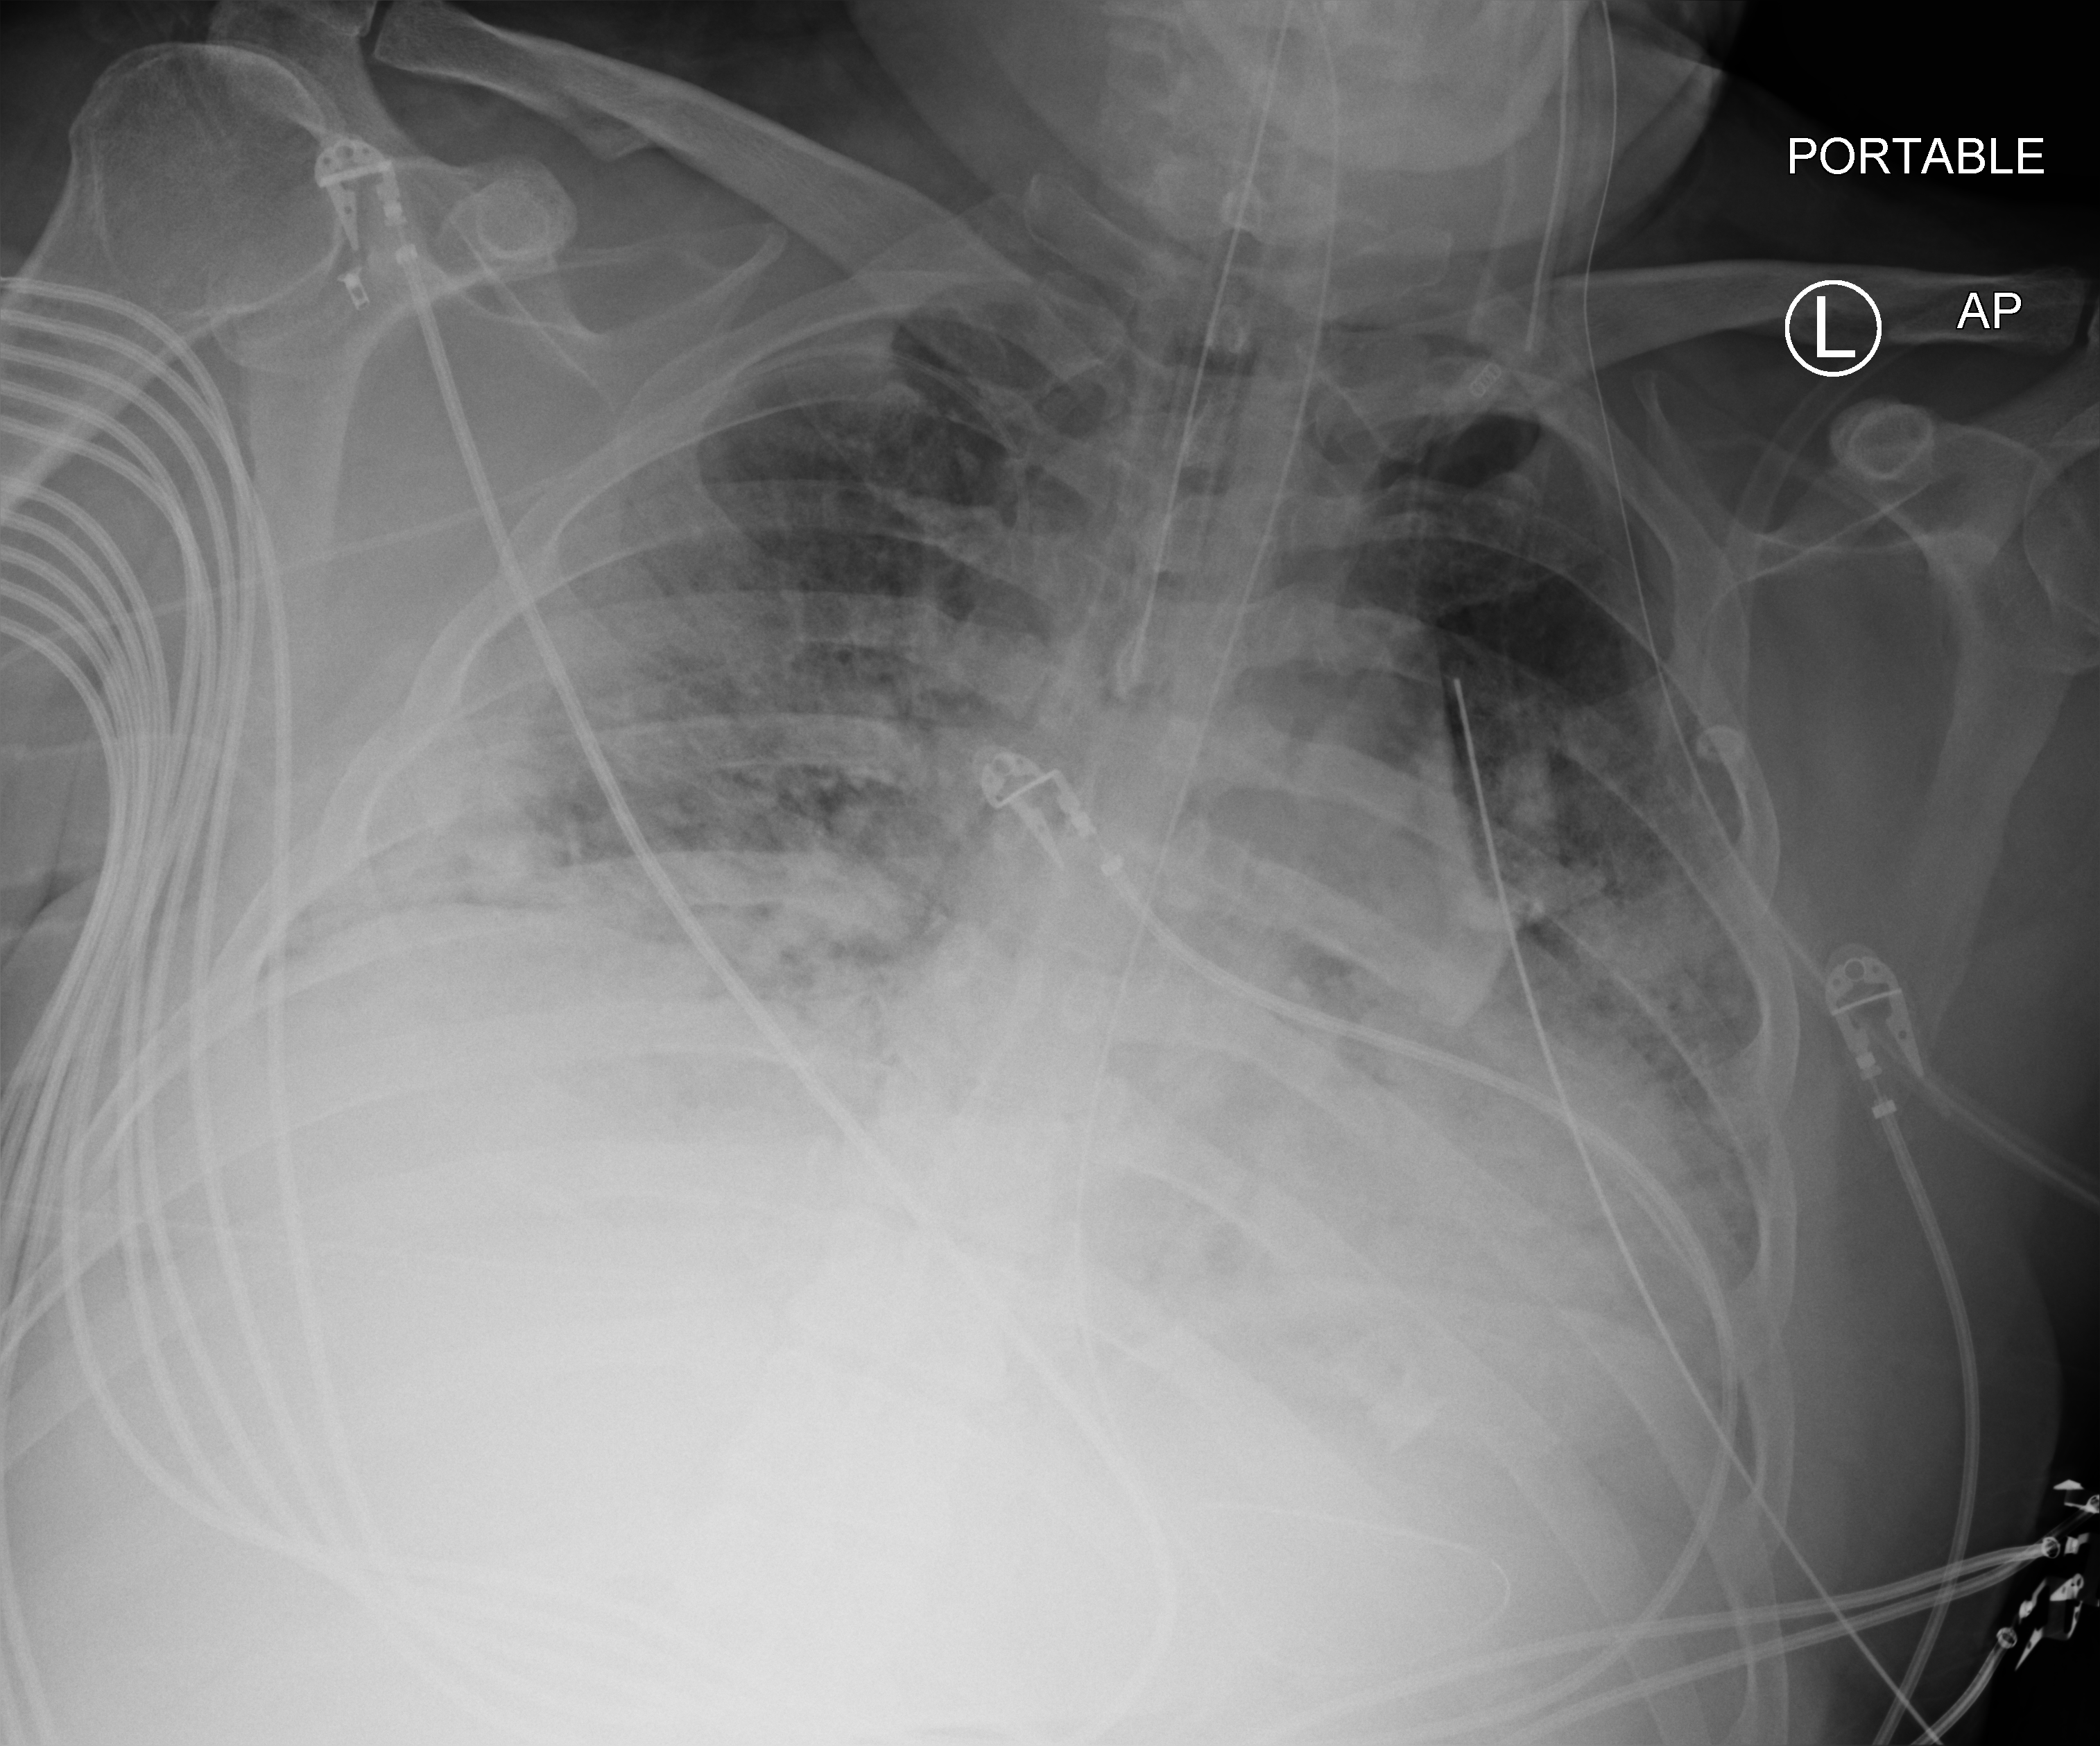
Chest X-ray (portable), anteroposterior (AP) projection. Patient hospitalised with COVID-19; male, aged 18–59 years.
From the hospital-stay record, not from the radiograph (when in the stay this image was taken is not recorded):
- diabetes (admission record): no
- mechanically ventilated during this hospital stay: yes
- admitted to intensive care during this hospital stay: yes